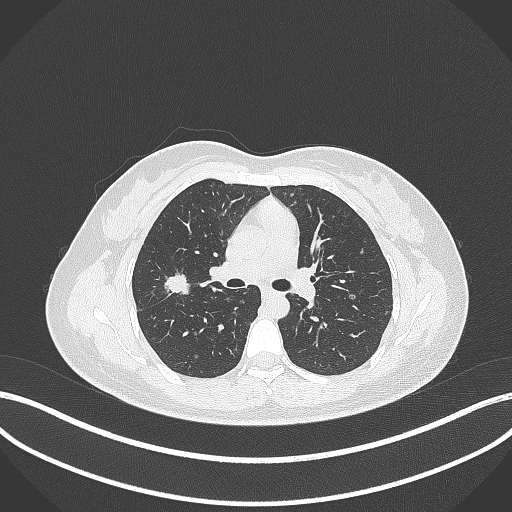
Chest CT, one axial slice. Position 202 of 307 along the scan axis. Lung window (W 1500 / L -600 HU). 1 mm slice thickness. 512 × 512 image matrix. Patient: female, 33 years. Case-level facts recorded for this patient, not image findings: clinical TNM (as recorded): T1c N0 M0; histopathological grade: G2-G3.
Outlined on this slice (rectangle marked by the reading radiologist):
- lung tumour (recorded histology: adenocarcinoma): bounding box [x1, y1, x2, y2] px = [160, 272, 193, 299]